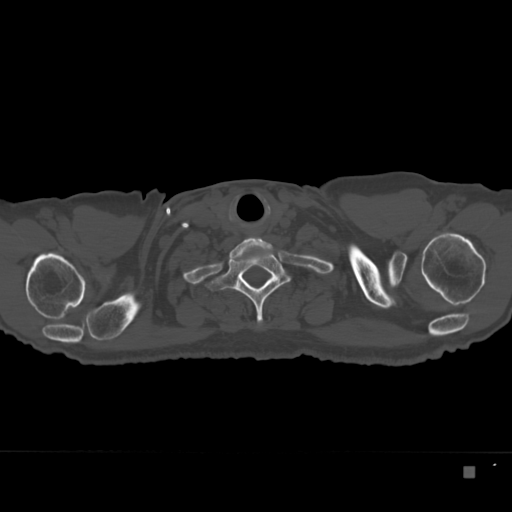
CT including the spine, one axial slice; position 317 of 332 along the scan axis; 120 kVp; bone window (W 1800 / L 400 HU); 512 × 512 image matrix, field of view 389 × 389 mm. Patient: male, 72 years. Case-level facts recorded for this patient, not image findings: primary cancer: skeletal.
Outlined on this slice (semi-automatic segmentation, software-assisted and operator-edited):
- T1 vertebra: bounding box [x1, y1, x2, y2] px = [206, 246, 290, 325]